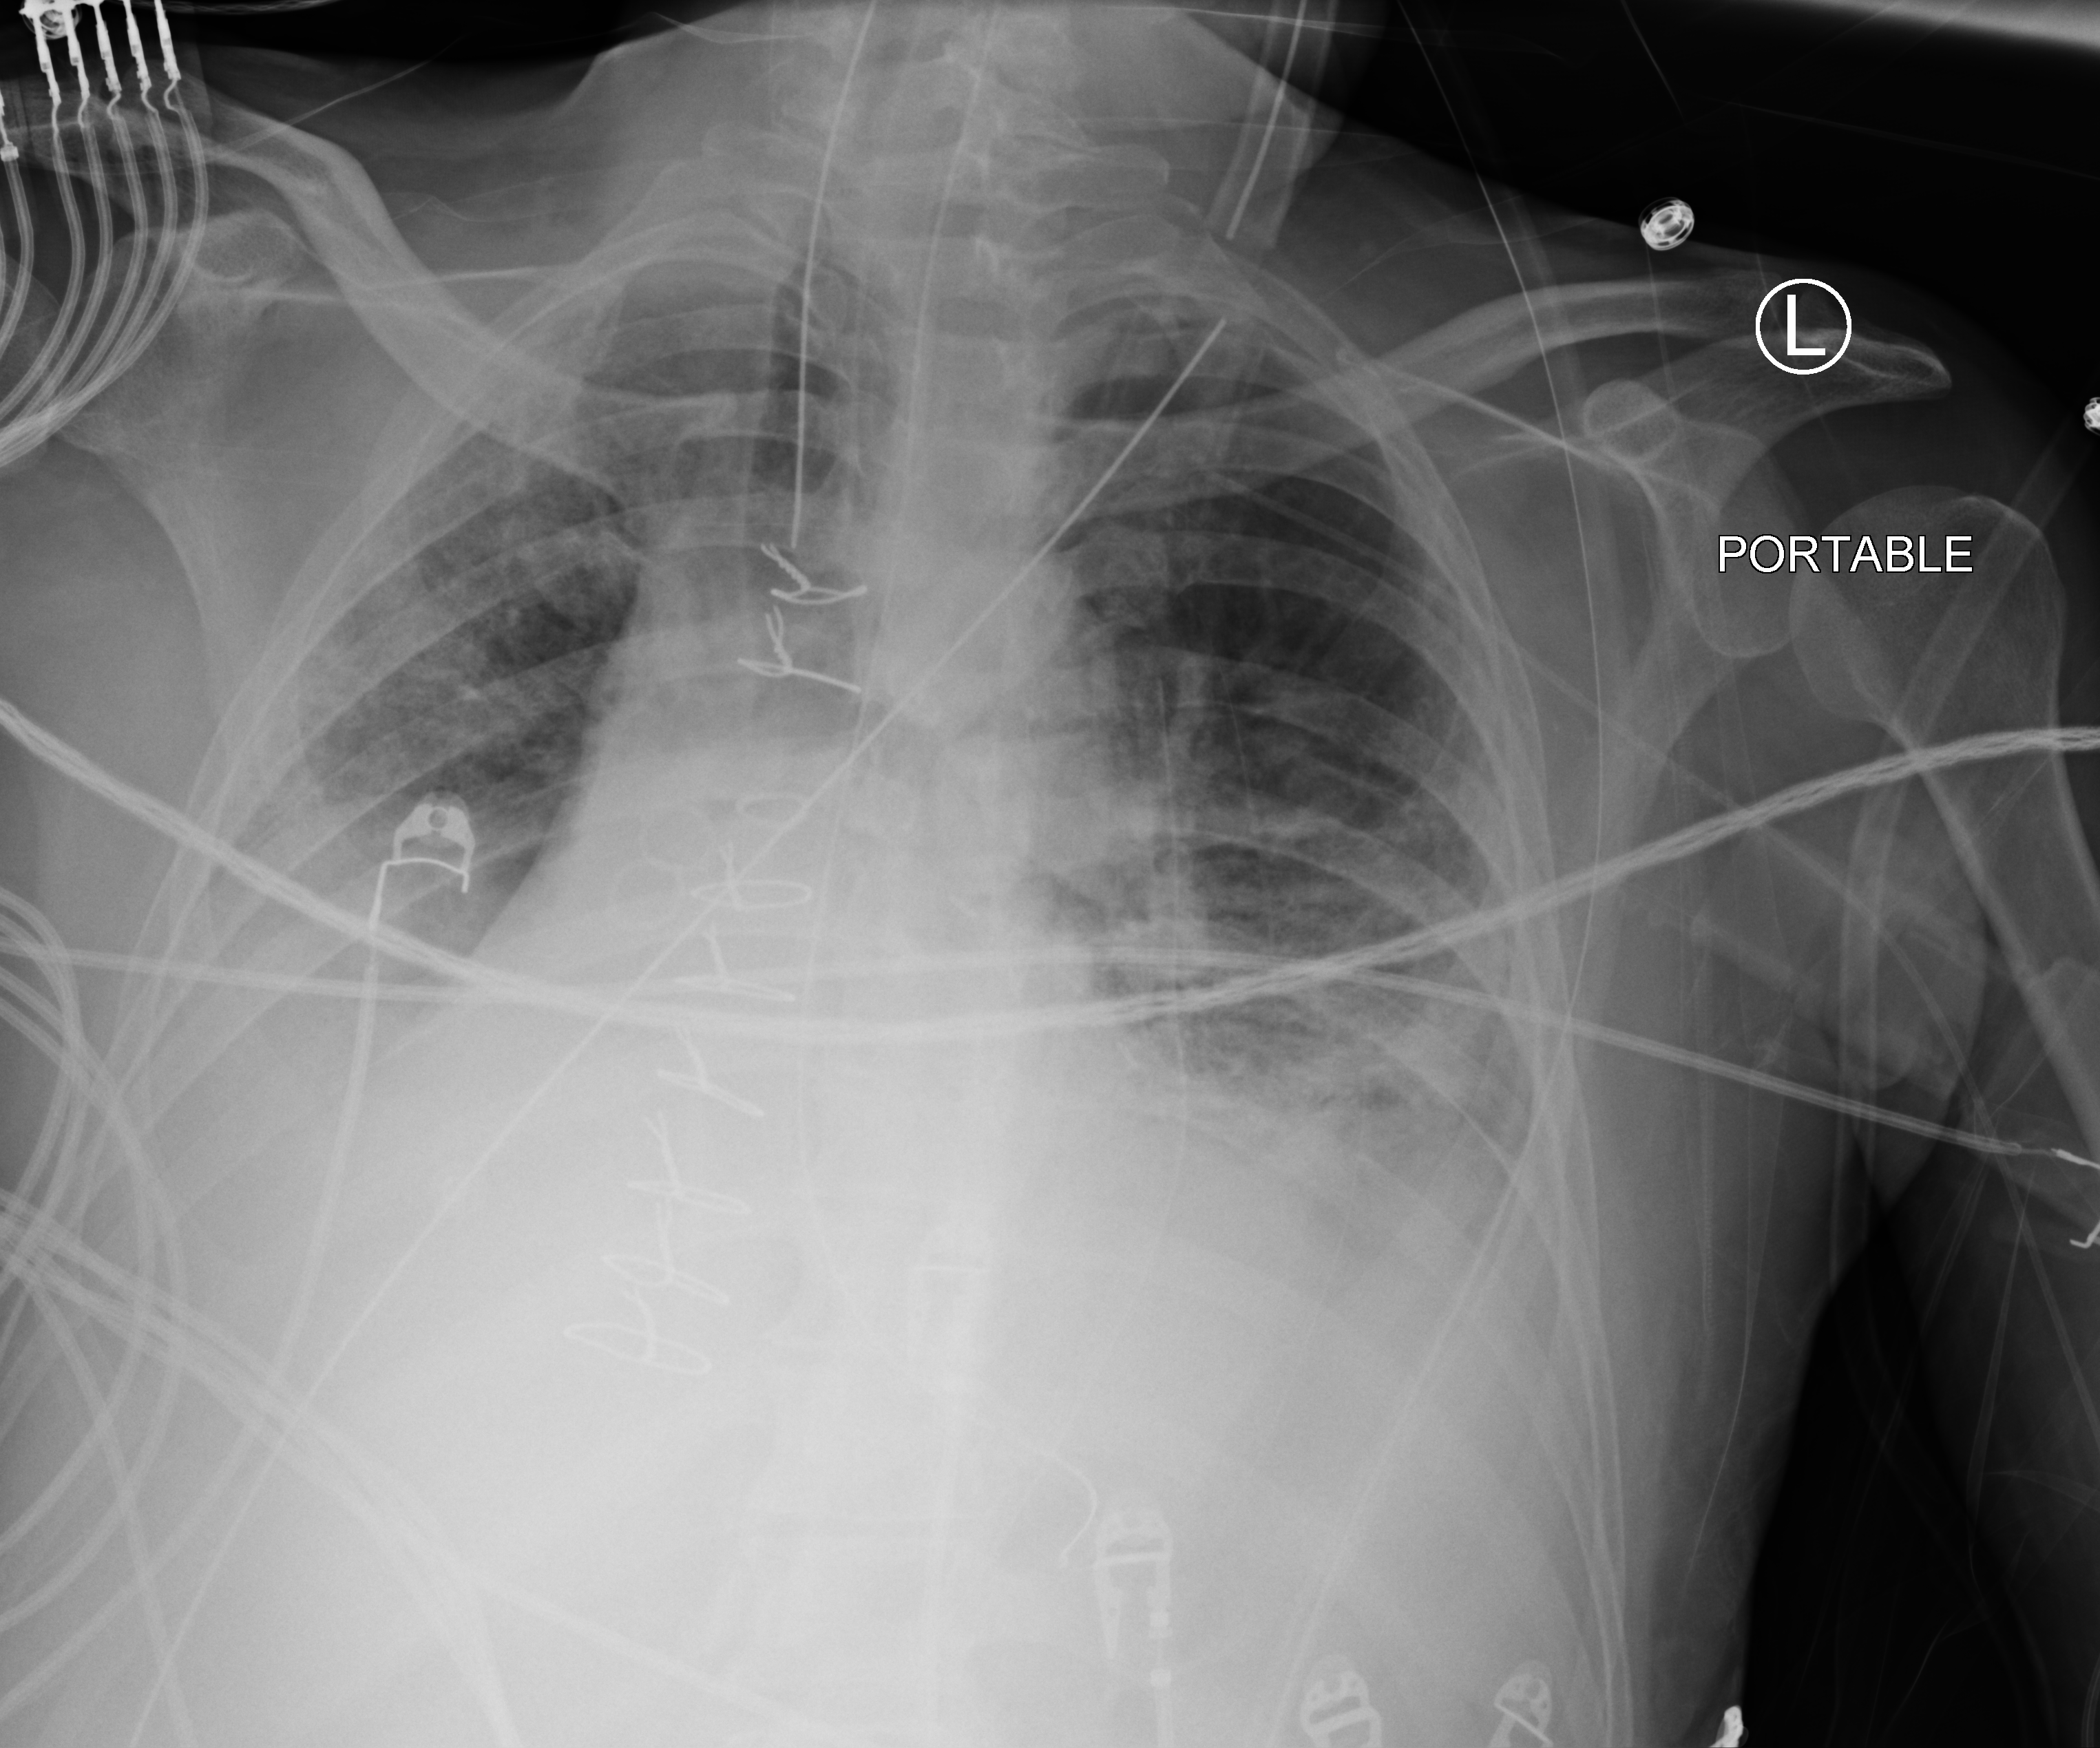
Chest X-ray (portable). Patient hospitalised with COVID-19; male, aged 18–59 years.
Admission-level facts for this patient (not findings on this image; timing relative to this image not recorded): admitted to intensive care during this hospital stay: yes.